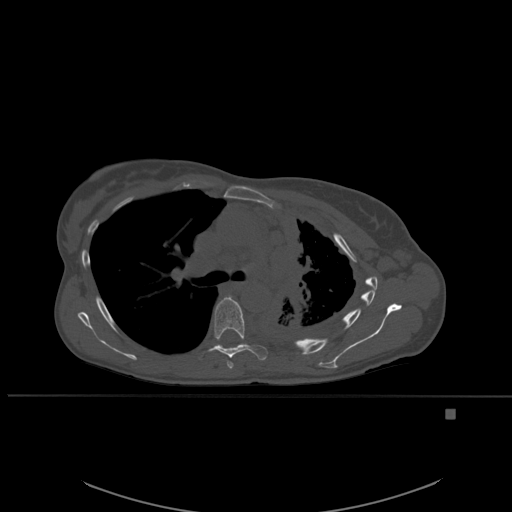
CT including the spine, one axial slice; slice 384 of 537 in the series (ordered by position); bone window (W 1800 / L 400 HU); 512 × 512 image matrix, field of view 440 × 440 mm. Female patient, age 45 years. From the clinical record (not read from this slice): primary cancer: lung.
Structures marked on this image (semi-automatic segmentation, software-assisted and operator-edited):
- T5 vertebra: box from (x=227, y=301) to (x=236, y=369) px
- T6 vertebra: (x=209, y=296)–(x=268, y=362)
- T7 vertebra: (x=220, y=344)–(x=242, y=346)